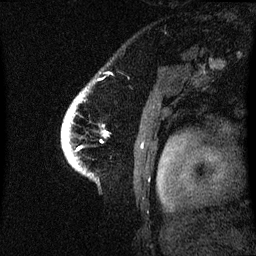
Breast MRI (dynamic contrast-enhanced), one sagittal slice; dynamic contrast-enhanced series, image 2 of 3 at this slice position (ordered by acquisition); 1.5 T; TE 4.2 ms, TR 8.4 ms; 2.1 mm slice thickness; 256 × 256 image matrix. Patient: female, 53 years. From the clinical record (not read from this slice): setting: breast cancer imaged before/during neoadjuvant chemotherapy; receptor status: HR-positive, HER2-negative.
Structures marked on this image (semi-automatically segmented with operator editing):
- analysis volume of interest (the breast-tissue region the enhancement analysis was run in; not a lesion): bounding box <63,102,83,171> (left, top, right, bottom; pixels)
- tumour enhancement mask (voxels above the 70 % enhancement threshold inside the analysis volume of interest): <65,132,69,139>